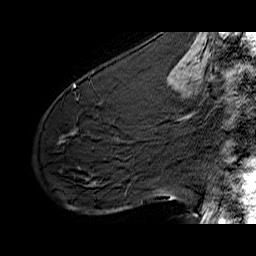
Breast MRI (dynamic contrast-enhanced), one sagittal slice. Position 36 of 60 along the scan axis. Dynamic contrast-enhanced series, time point 2 of 6 at this slice position (early post-contrast). 1.5 T. TE 6.4 ms, TR 32.9 ms. 4 mm slice thickness. 256 × 256 image matrix, field of view 200 × 200 mm. Female patient. Case-level facts recorded for this patient, not image findings: setting: breast cancer imaged before/during neoadjuvant chemotherapy; receptor status: HER2-positive.
Annotated regions visible in this slice (semi-automatically segmented with operator editing):
- analysis volume of interest (the breast-tissue region the enhancement analysis was run in; not a lesion): box from (x=61, y=77) to (x=141, y=142) px
- tumour enhancement mask (voxels above the 100 % enhancement threshold inside the analysis volume of interest): (x=73, y=85)–(x=76, y=87)